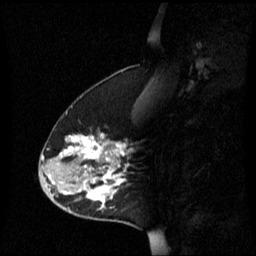
Breast MRI (dynamic contrast-enhanced), one sagittal slice; slice 22 of 60 in the series (ordered by position); dynamic contrast-enhanced series, image 2 of 3 at this slice position (ordered by acquisition); 1.5 T; TE 4.2 ms, TR 8.4 ms; 256 × 256 image matrix, field of view 240 × 240 mm. Female patient, age 45 years. Case-level facts recorded for this patient, not image findings: setting: breast cancer imaged before/during neoadjuvant chemotherapy; receptor status: HR-positive, HER2-negative.
Structures marked on this image (semi-automatically segmented with operator editing):
- analysis volume of interest (the breast-tissue region the enhancement analysis was run in; not a lesion): bounding box <40,132,131,221> (left, top, right, bottom; pixels)
- tumour enhancement mask (voxels above the 70 % enhancement threshold inside the analysis volume of interest): <48,134,129,207>